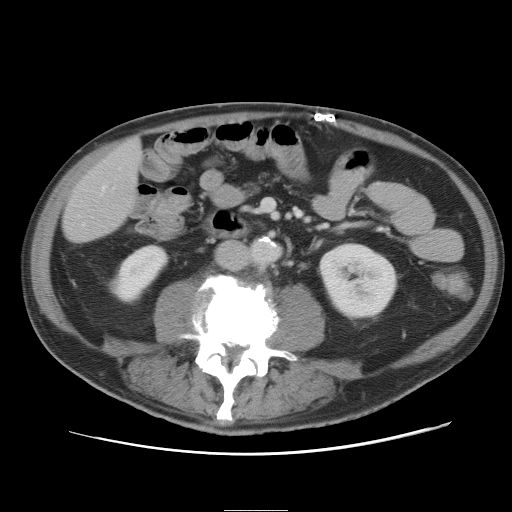
Contrast-enhanced abdominal CT, one axial slice; position 7 of 89 along the scan axis; intravenous contrast given; soft-tissue window (W 400 / L 40 HU); 5 mm slice thickness; 512 × 512 image matrix. Male patient, age 69 years. From the clinical record (not read from this slice): diagnosis: colorectal cancer liver metastases, imaged before liver resection; multiple liver metastases: no; largest metastasis: 8.5 cm; chemotherapy before resection: no.
Structures marked on this image (manually delineated by an expert):
- hepatic veins: bounding box <103,186,105,189> (left, top, right, bottom; pixels)
- liver: <64,138,143,242>
- planned liver remnant (the part of the liver to remain after resection): <64,139,142,242>